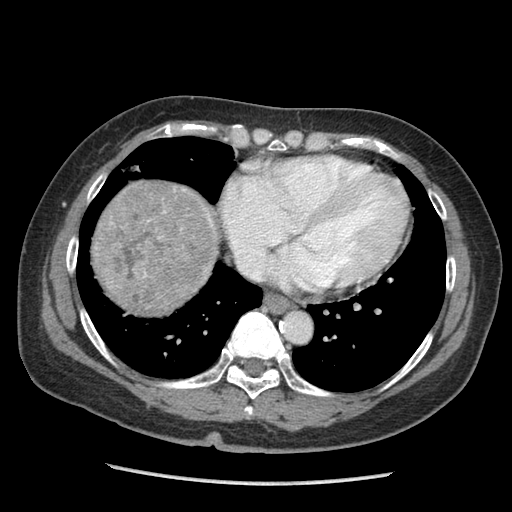
Contrast-enhanced abdominal CT (liver protocol), one axial slice; position 91 of 105 along the scan axis; soft-tissue window (W 400 / L 40 HU); 2.5 mm slice thickness; 512 × 512 image matrix, field of view 340 × 340 mm. From the clinical record (not read from this slice): diagnosis: hepatocellular carcinoma (patient treated with transarterial chemoembolisation; whether this scan precedes or follows treatment is not stated here); TNM stage (as recorded): Stage-I; Child-Pugh class: A; tumour differentiation: moderately differentiated; tumour nodularity: uninodular.
Outlined on this slice (semi-automatic segmentation, software-assisted and operator-edited):
- liver parenchyma outside the tumour (the mass and vessels are separate outlines, so this box may not span the whole liver): bounding box [x1, y1, x2, y2] px = [92, 180, 212, 314]
- mass: [96, 183, 220, 315]